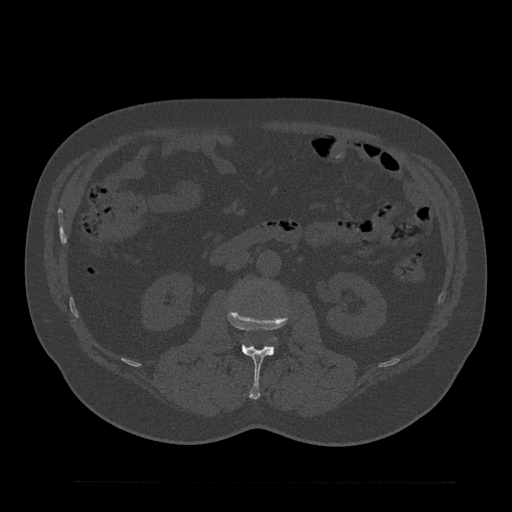
CT including the spine, one axial slice; slice 82 of 797 in the series (ordered by position); reconstruction kernel Br40s/3; 120 kVp; bone window (W 1800 / L 400 HU); 0.5 mm slice thickness; 512 × 512 image matrix. Patient: male, 61 years. From the clinical record (not read from this slice): primary cancer: prostate.
Structures marked on this image (semi-automatic segmentation, software-assisted and operator-edited):
- L2 vertebra: bounding box <227,308,289,400> (left, top, right, bottom; pixels)